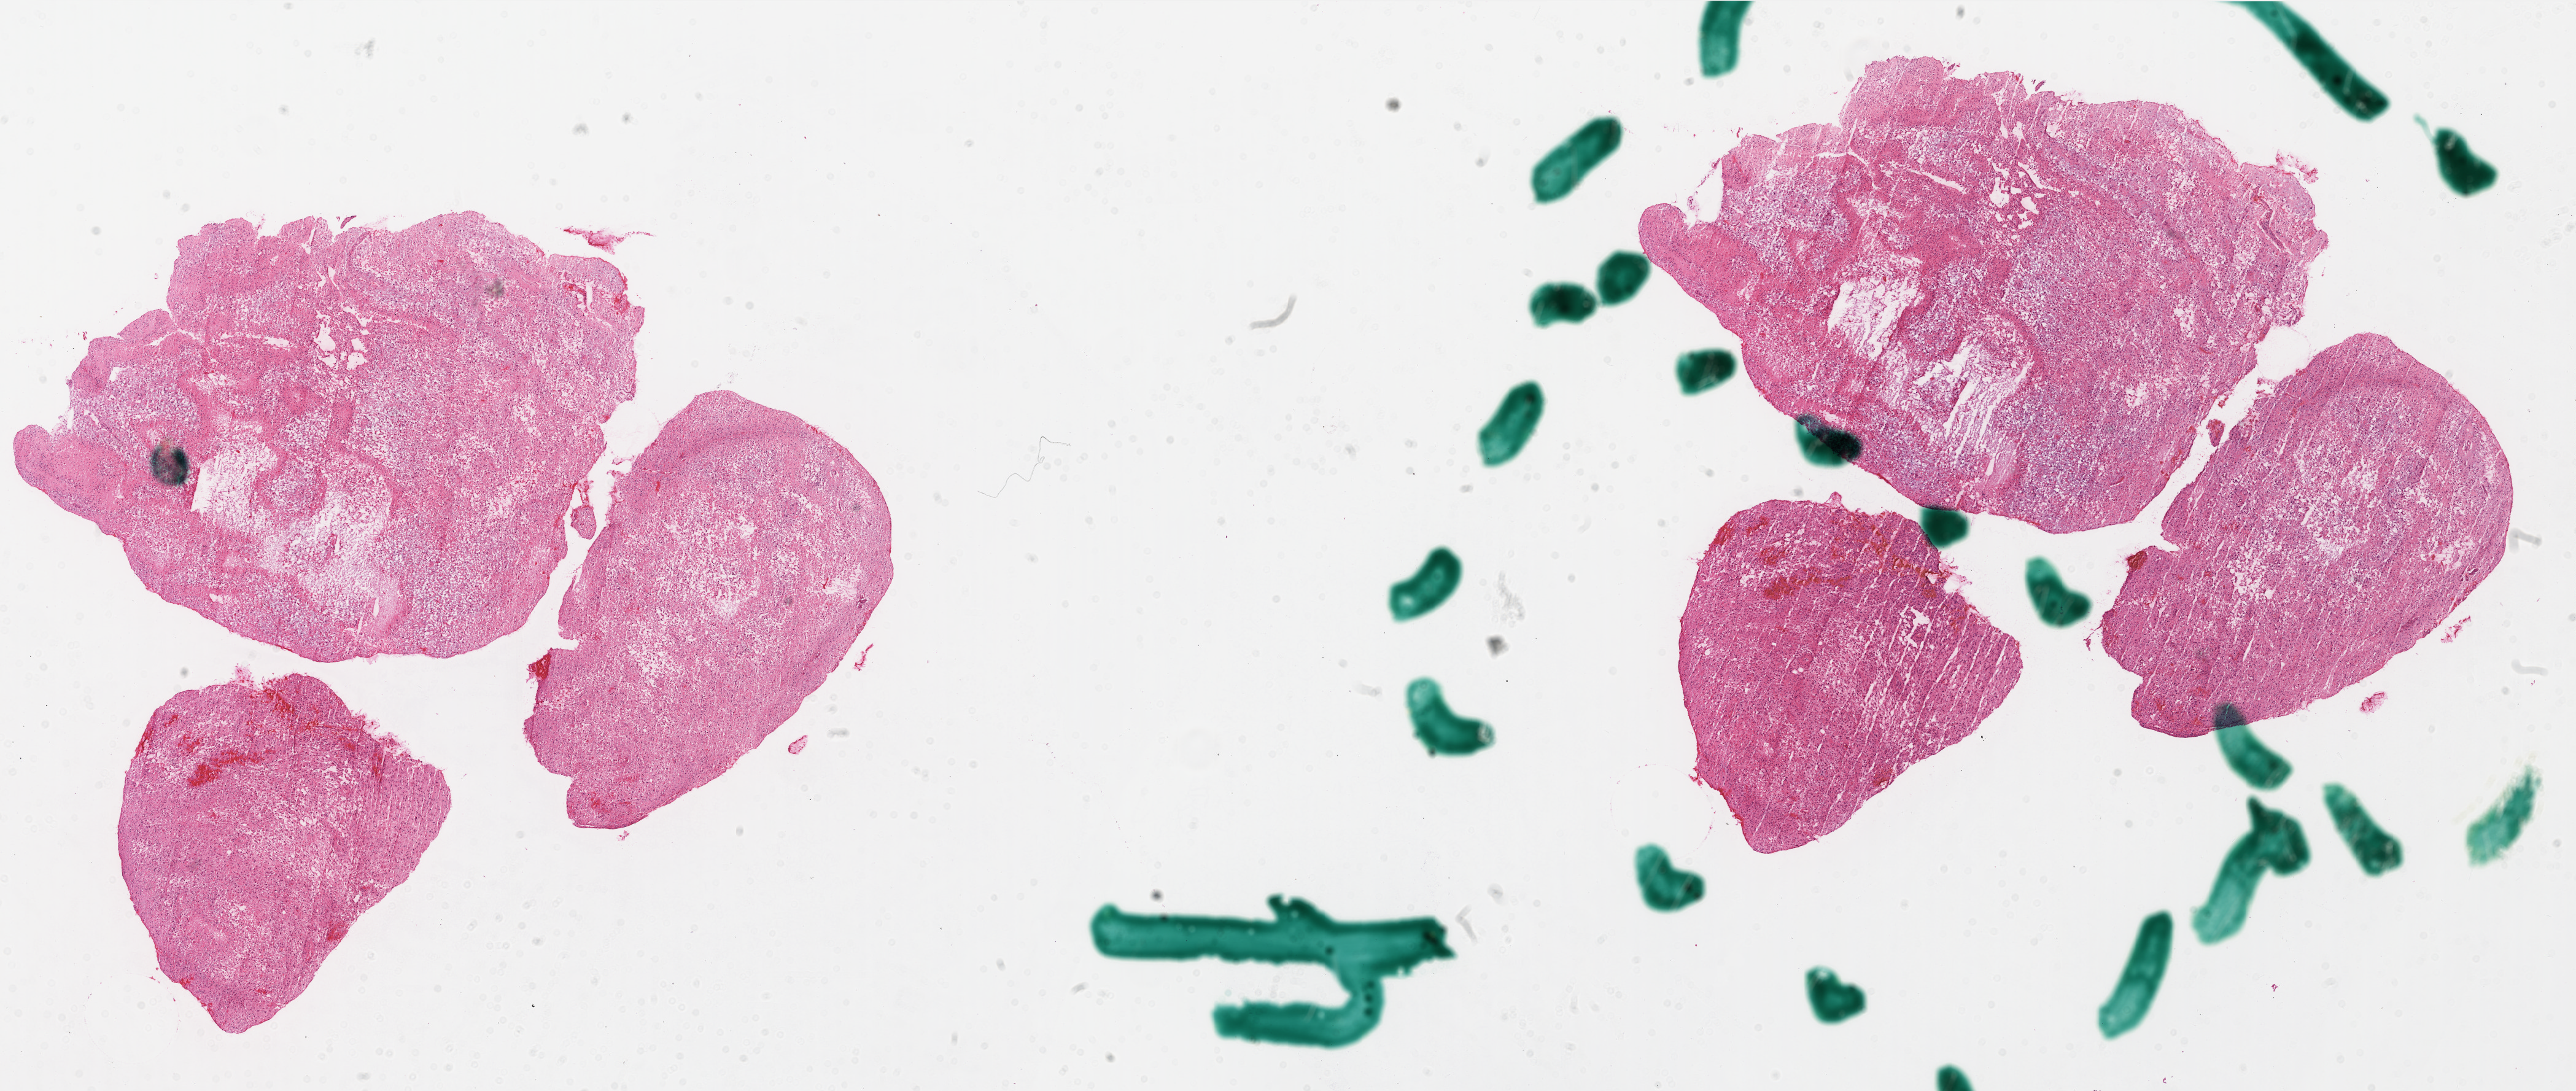
Whole-slide histology image, H&E-stained, shown as a low-resolution overview of the whole scanned area (about 33.7 x 14.3 mm, from a 20x scan), frozen section, primary tumour sample from the brain. Patient: male, age at initial diagnosis 54 years. Pathologist review of this section (percent, as recorded): tumour cells 80%, tumour nuclei 100%, normal cells 0%, stromal cells 0%, necrosis 20%.
Histologic diagnosis: Glioblastoma.